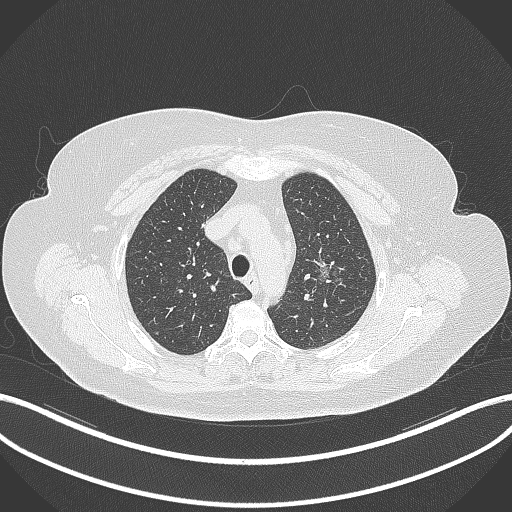
Chest CT, one axial slice. Slice 260 of 309 in the series (ordered by position). Reconstruction kernel B70f. Lung window (W 1500 / L -600 HU). 1 mm slice thickness. 512 × 512 image matrix. Female patient, age 70 years. From the clinical record (not read from this slice): clinical TNM (as recorded): T1c N0 M0.
Annotated regions visible in this slice (bounding box drawn by a radiologist):
- lung tumour (recorded histology: adenocarcinoma): bounding box <310,256,345,296> (left, top, right, bottom; pixels)